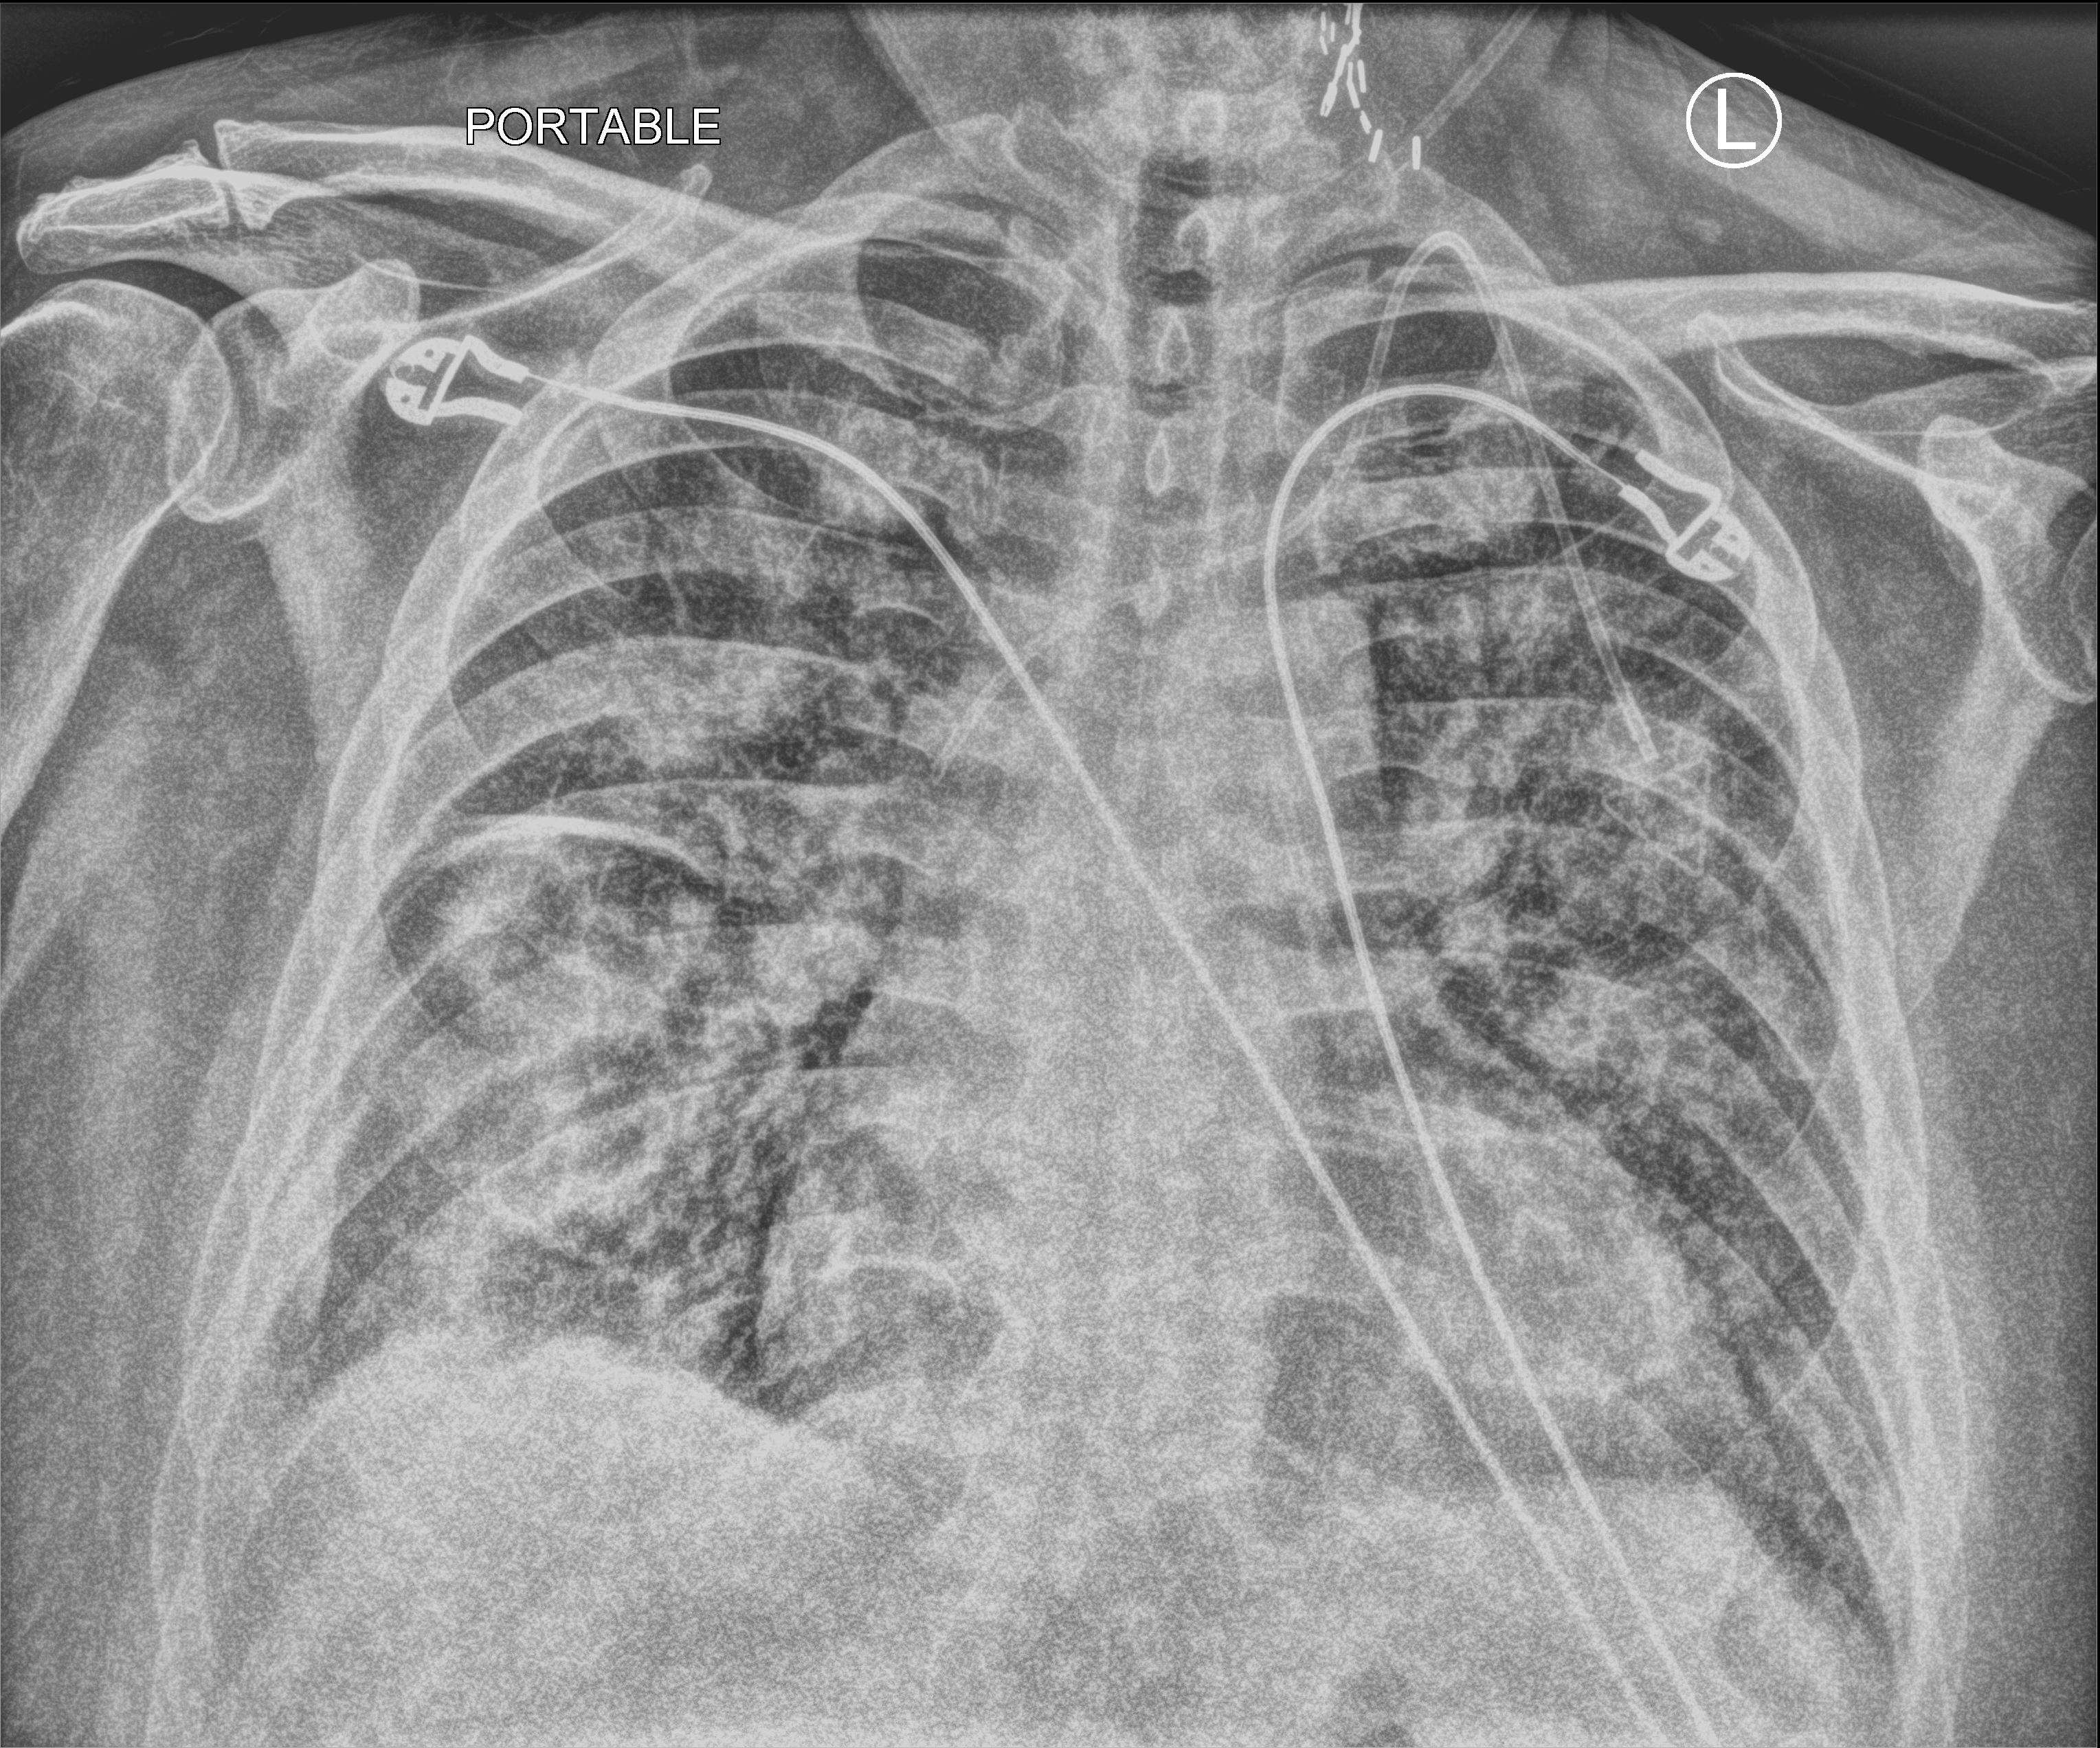
Portable chest radiograph. Male patient hospitalised with COVID-19, age 60–74 years.
Hospital-stay facts (about this admission, not read from this image; timing relative to this image not recorded):
- mechanically ventilated during this hospital stay: no
- length of hospital stay: 4 days
- admitted to intensive care during this hospital stay: no